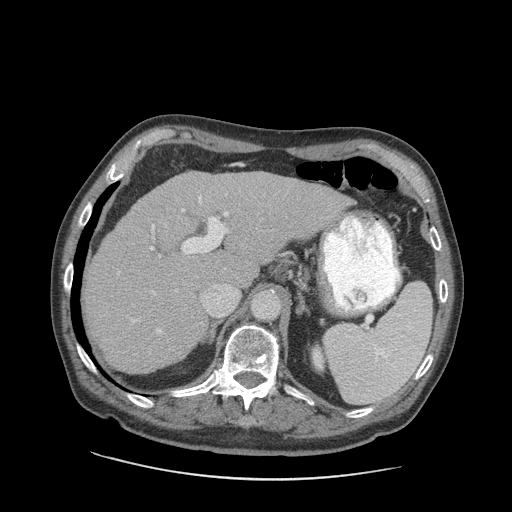
Contrast-enhanced abdominal CT (liver protocol), one axial slice; slice 60 of 89 in the series (ordered by position); 140 kVp; soft-tissue window (W 400 / L 40 HU); 2.5 mm slice thickness; 512 × 512 image matrix, field of view 420 × 420 mm. From the clinical record (not read from this slice): diagnosis: hepatocellular carcinoma (patient treated with transarterial chemoembolisation; whether this scan precedes or follows treatment is not stated here); TNM stage (as recorded): Stage-I; Child-Pugh class: A; tumour differentiation: moderately differentiated; tumour nodularity: uninodular.
Outlined on this slice (semi-automatic segmentation, software-assisted and operator-edited):
- liver parenchyma outside the tumour (the mass and vessels are separate outlines, so this box may not span the whole liver): bounding box (x1, y1, x2, y2) in pixels: (84, 170, 351, 374)
- liver vessels: (117, 191, 288, 333)